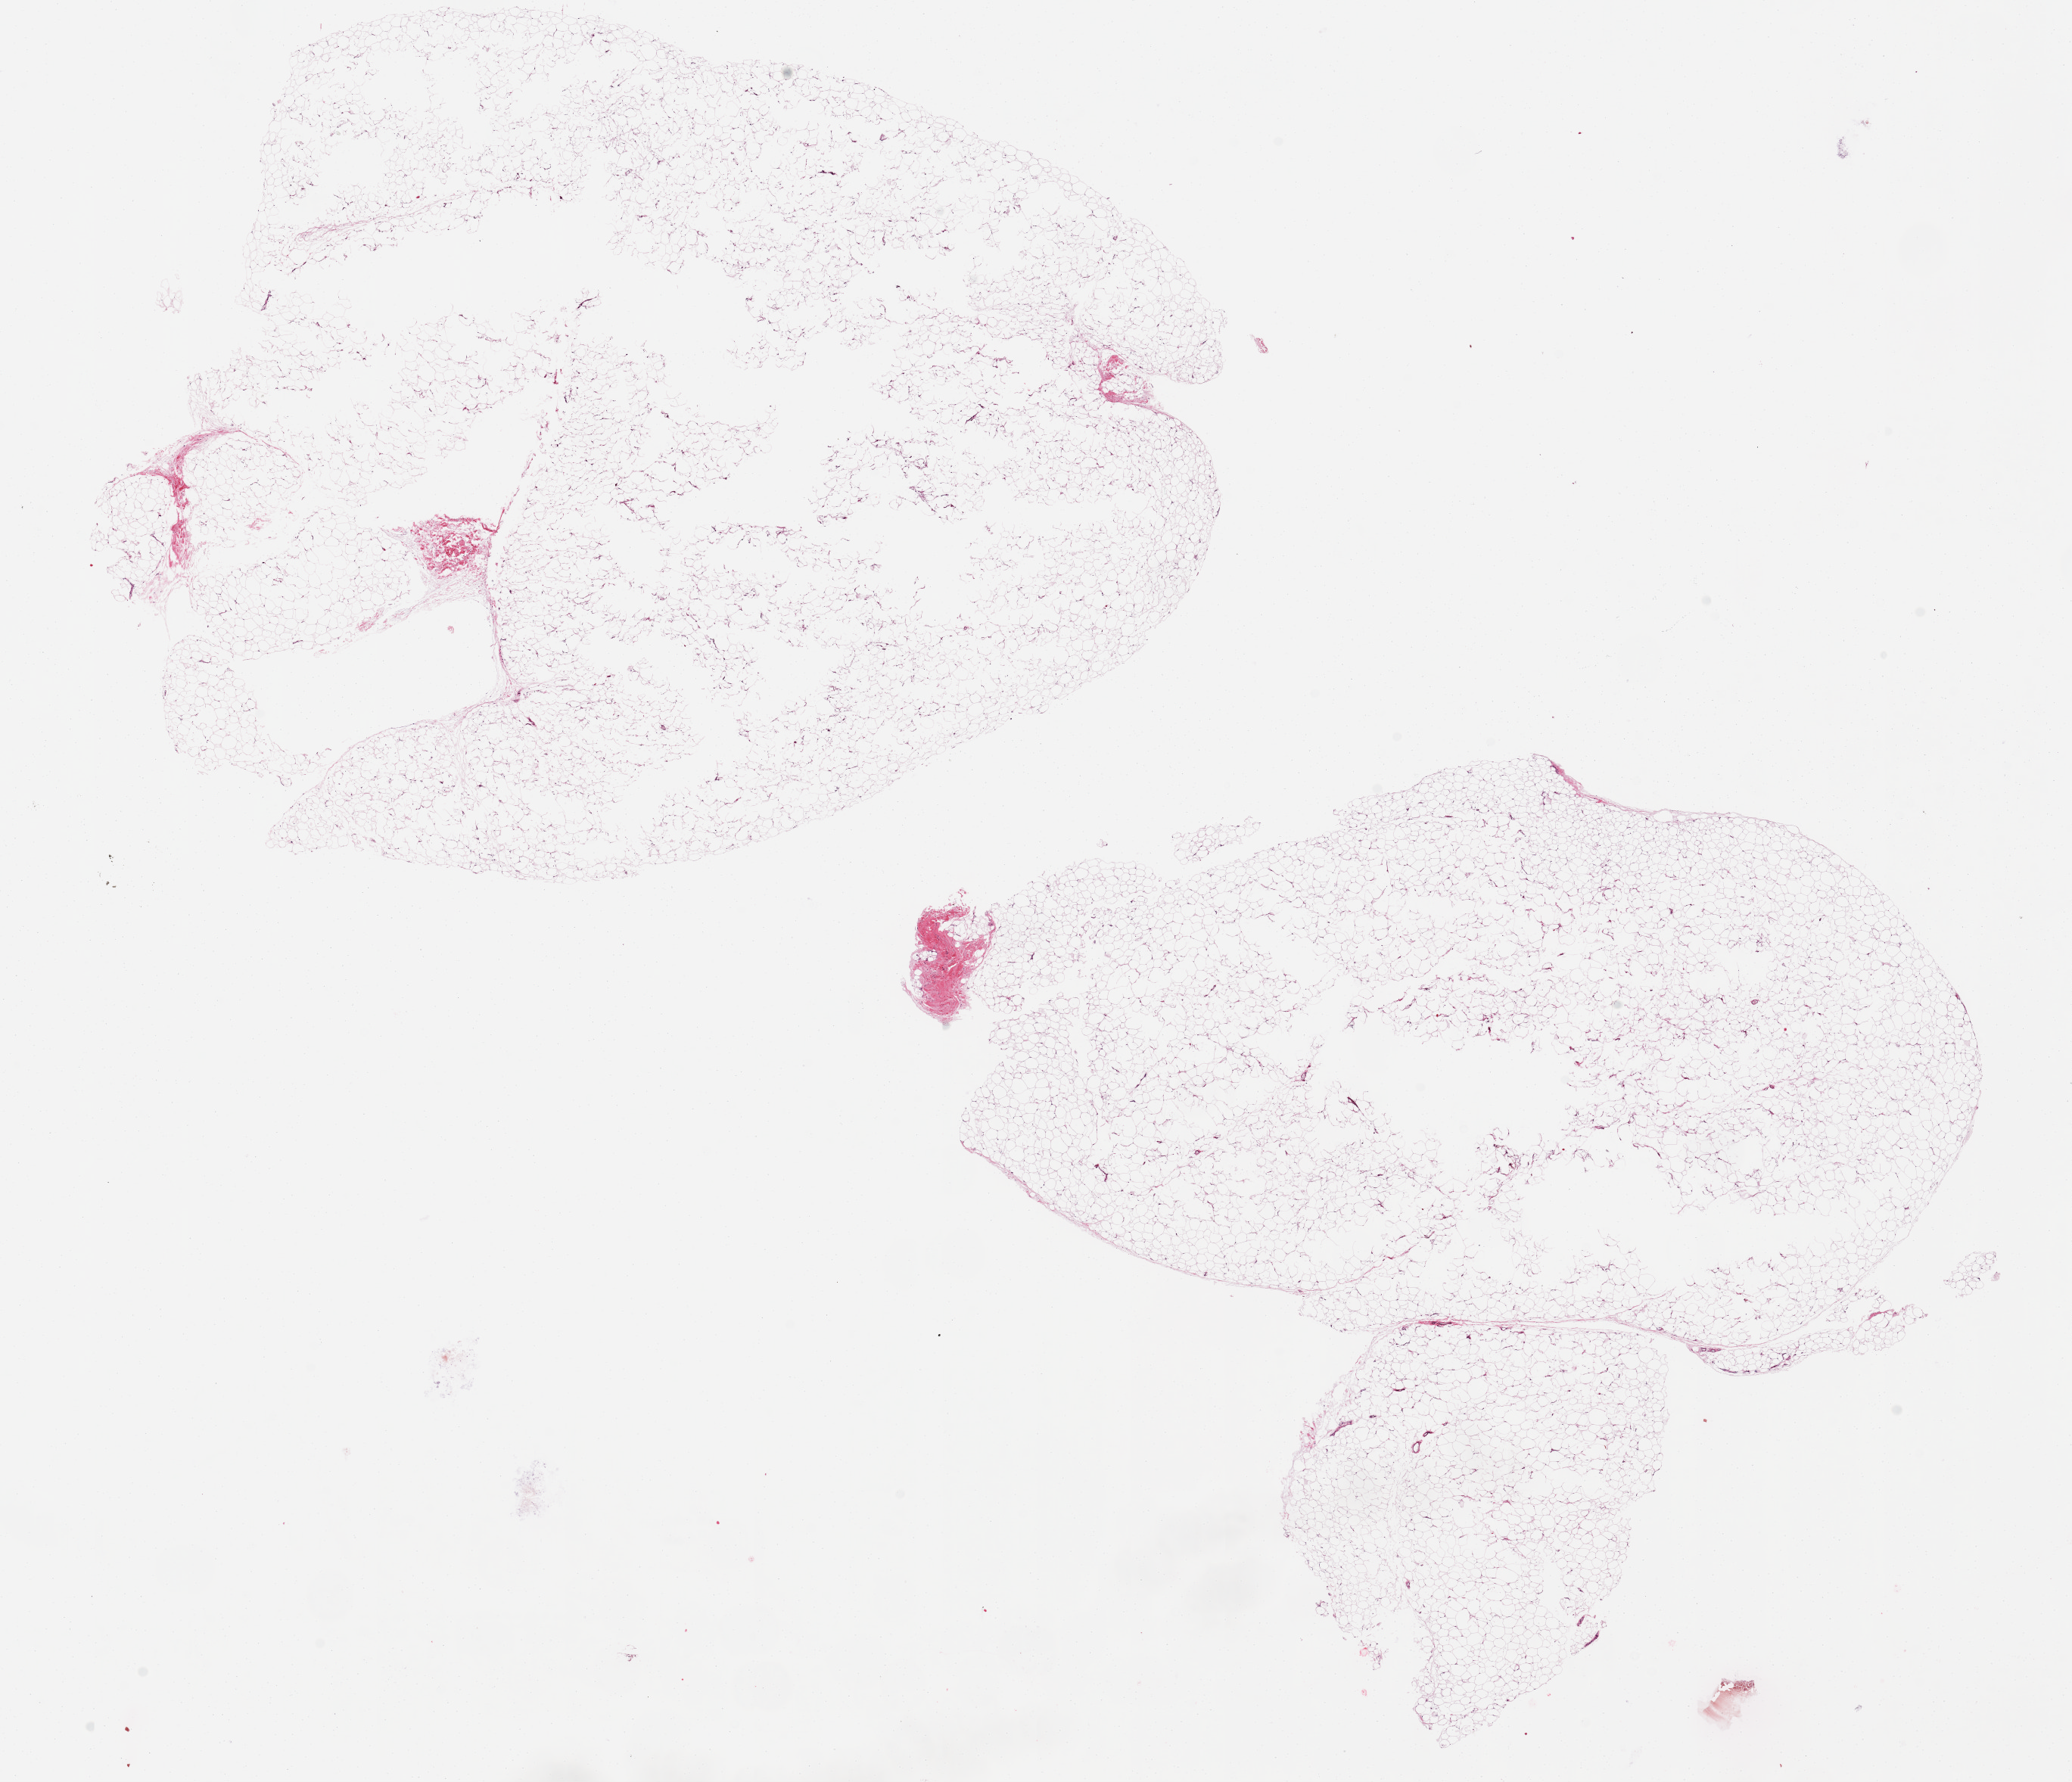
H&E whole-slide image, a low-resolution overview of the entire scanned area, about 21.7 x 18.6 mm. PAXgene-fixed paraffin-embedded (PFPE) section. Sampled site (target tissue): adipose tissue. Donor tissue sample.
- pathologist's review note for this sample: 2 pieces up to 11x9mm; central defects from poor fixation